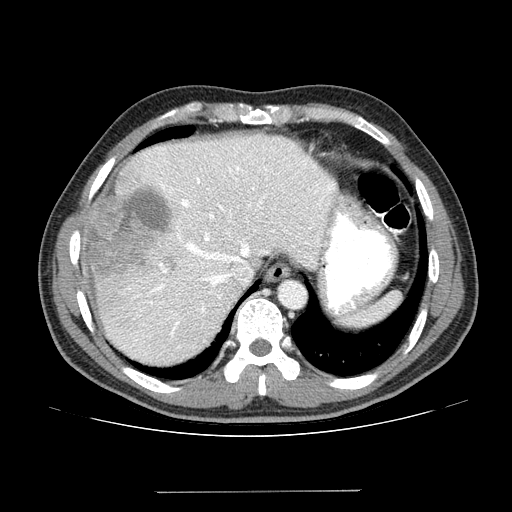
Contrast-enhanced abdominal CT (liver protocol), one axial slice; slice 108 of 131 in the series (ordered by position); one of 2 acquisitions stored at this slice position; soft-tissue window (W 400 / L 40 HU); 2.5 mm slice thickness; 512 × 512 image matrix, field of view 380 × 380 mm. Case-level facts recorded for this patient, not image findings: diagnosis: hepatocellular carcinoma (patient treated with transarterial chemoembolisation; whether this scan precedes or follows treatment is not stated here); TNM stage (as recorded): Stage-I; Child-Pugh class: A; tumour differentiation: poorly differentiated; tumour nodularity: uninodular.
Outlined on this slice (semi-automatically segmented with operator editing):
- abdominal aorta: bounding box <280,282,305,308> (left, top, right, bottom; pixels)
- liver parenchyma outside the tumour (the mass and vessels are separate outlines, so this box may not span the whole liver): <80,134,336,364>
- mass: <81,183,173,286>
- liver vessels: <123,145,335,355>